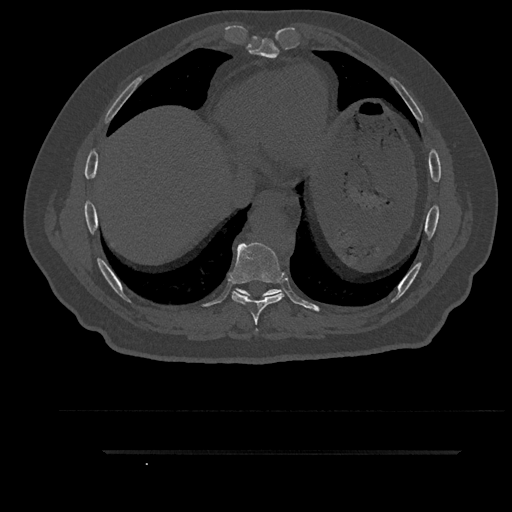
CT including the spine, one axial slice. Slice 461 of 797 in the series (ordered by position). Reconstruction kernel Br40s/3. 120 kVp. Bone window (W 1800 / L 400 HU). 512 × 512 image matrix, field of view 432 × 432 mm. Patient: male, 63 years. Case-level facts recorded for this patient, not image findings: primary cancer: renal; vertebrae with lytic lesions (as recorded): T8.
Structures marked on this image (semi-automatic segmentation, software-assisted and operator-edited):
- T7 vertebra: bounding box <255,329,257,331> (left, top, right, bottom; pixels)
- T8 vertebra: <231,242,285,325>
- T9 vertebra: <235,288,282,298>